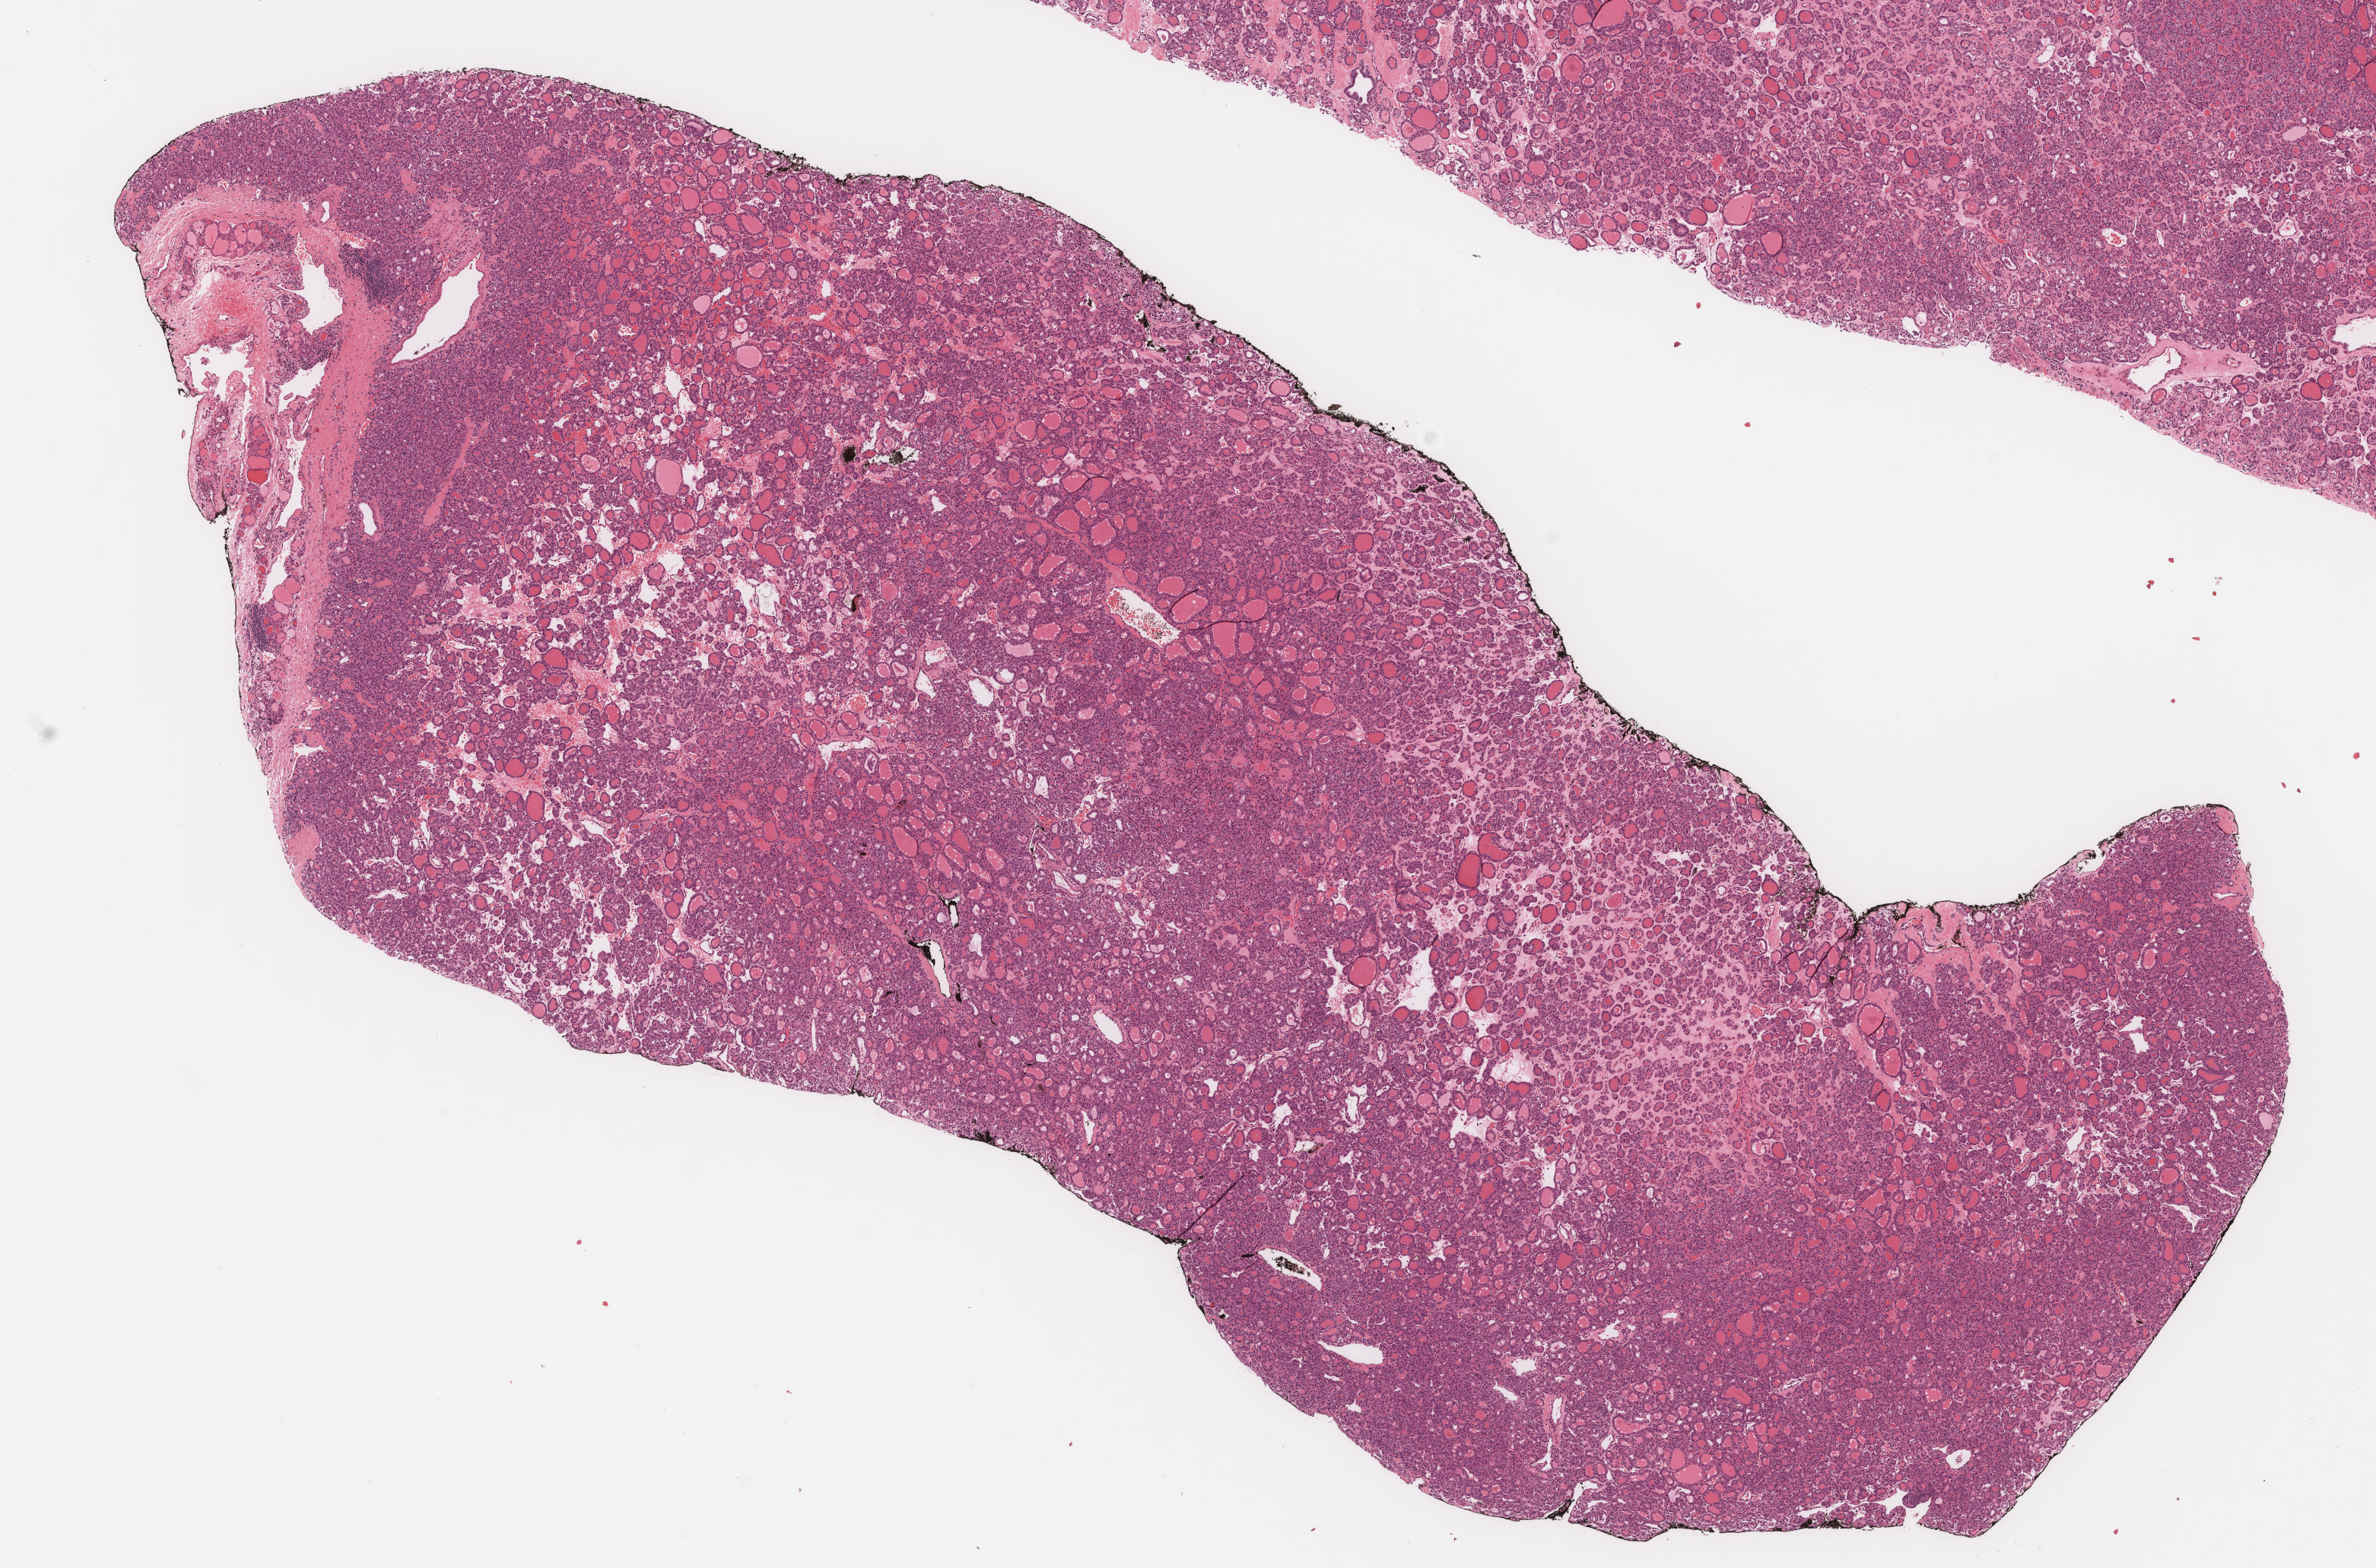
Whole-slide histology image, H&E — a low-resolution overview of the entire scanned area, about 12.6 x 8.3 mm (acquisition: 40x scan), formalin-fixed paraffin-embedded (FFPE) diagnostic section, primary tumour sample from the thyroid. Female patient; age at initial diagnosis 71 years.
Diagnosis: Papillary carcinoma, follicular variant (thyroid gland).